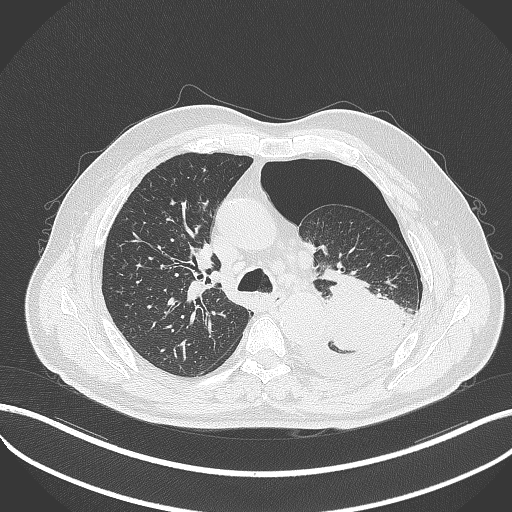
Chest CT, one axial slice; position 345 of 464 along the scan axis; reconstruction kernel B70f; 120 kVp; lung window (W 1500 / L -600 HU); 1 mm slice thickness; 512 × 512 image matrix, field of view 400 × 400 mm. Male patient, age 76 years. From the clinical record (not read from this slice): clinical TNM (as recorded): T3 N0 M1b.
Annotated regions visible in this slice (bounding box drawn by a radiologist):
- lung tumour (recorded histology: adenocarcinoma): bounding box [x1, y1, x2, y2] px = [319, 267, 405, 352]